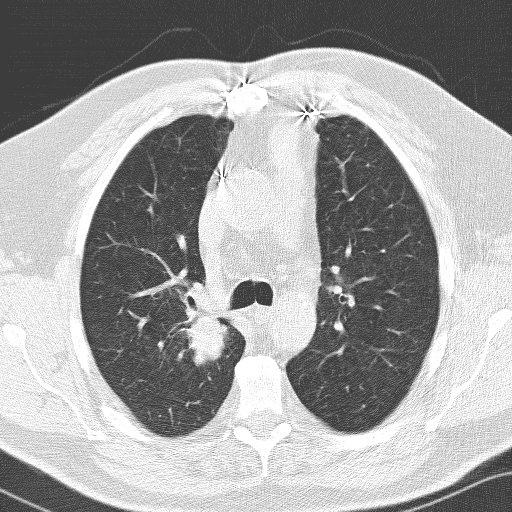
Low-dose screening chest CT, one axial slice. Position 102 of 141 along the scan axis. Lung window (W 1500 / L -600 HU). 3.2 mm slice thickness. 512 × 512 image matrix, field of view 326 × 326 mm.
Outlined on this slice (manually delineated by an expert):
- lesion 1 (tumor, upper lobe of right lung): bounding box <186,318,227,365> (left, top, right, bottom; pixels)